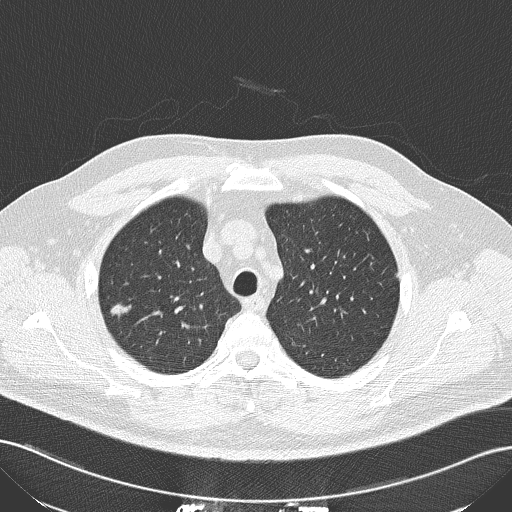
Axial slice from a low-dose chest CT screening exam, second annual screen, lung window (W 1500 / L -600 HU), 2 mm slice thickness. Male participant, aged 56 years at enrolment. Current smoker at enrolment.
- Lesion marked by an expert reader, box from (x=96, y=289) to (x=143, y=331) px.
- The exam's reader record, not a measurement of the box and not confirmed to be the same lesion: non-calcified nodule or mass ≥4 mm, right upper lobe, 10 × 9 mm, spiculated (stellate) margins, soft tissue attenuation, pre-existing on the prior screen: no.
- Official screen result: positive, other.
- Later outcome: lung cancer diagnosed 117 days after this screen — squamous cell carcinoma, NOS, right upper lobe, moderately differentiated (G2), stage IA (AJCC 6th edition), 10 mm at pathology.